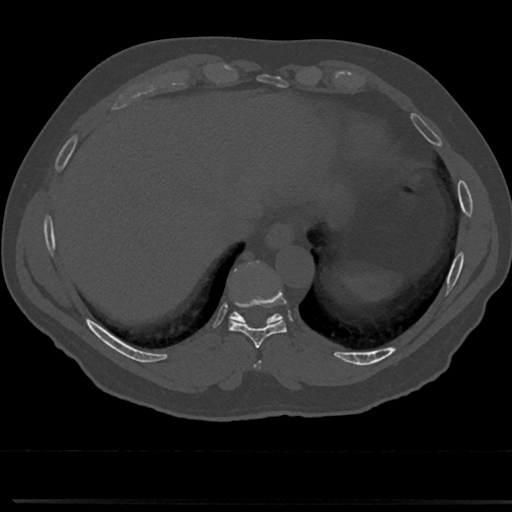
CT including the spine, one axial slice; position 292 of 817 along the scan axis; reconstruction kernel Br40s/3; 120 kVp; bone window (W 1800 / L 400 HU); 0.5 mm slice thickness; 512 × 512 image matrix, field of view 355 × 355 mm. Patient: male, 61 years. From the clinical record (not read from this slice): primary cancer: prostate.
Annotated regions visible in this slice (semi-automatically segmented with operator editing):
- T8 vertebra: bounding box <254,339,266,363> (left, top, right, bottom; pixels)
- T9 vertebra: <214,265,301,349>